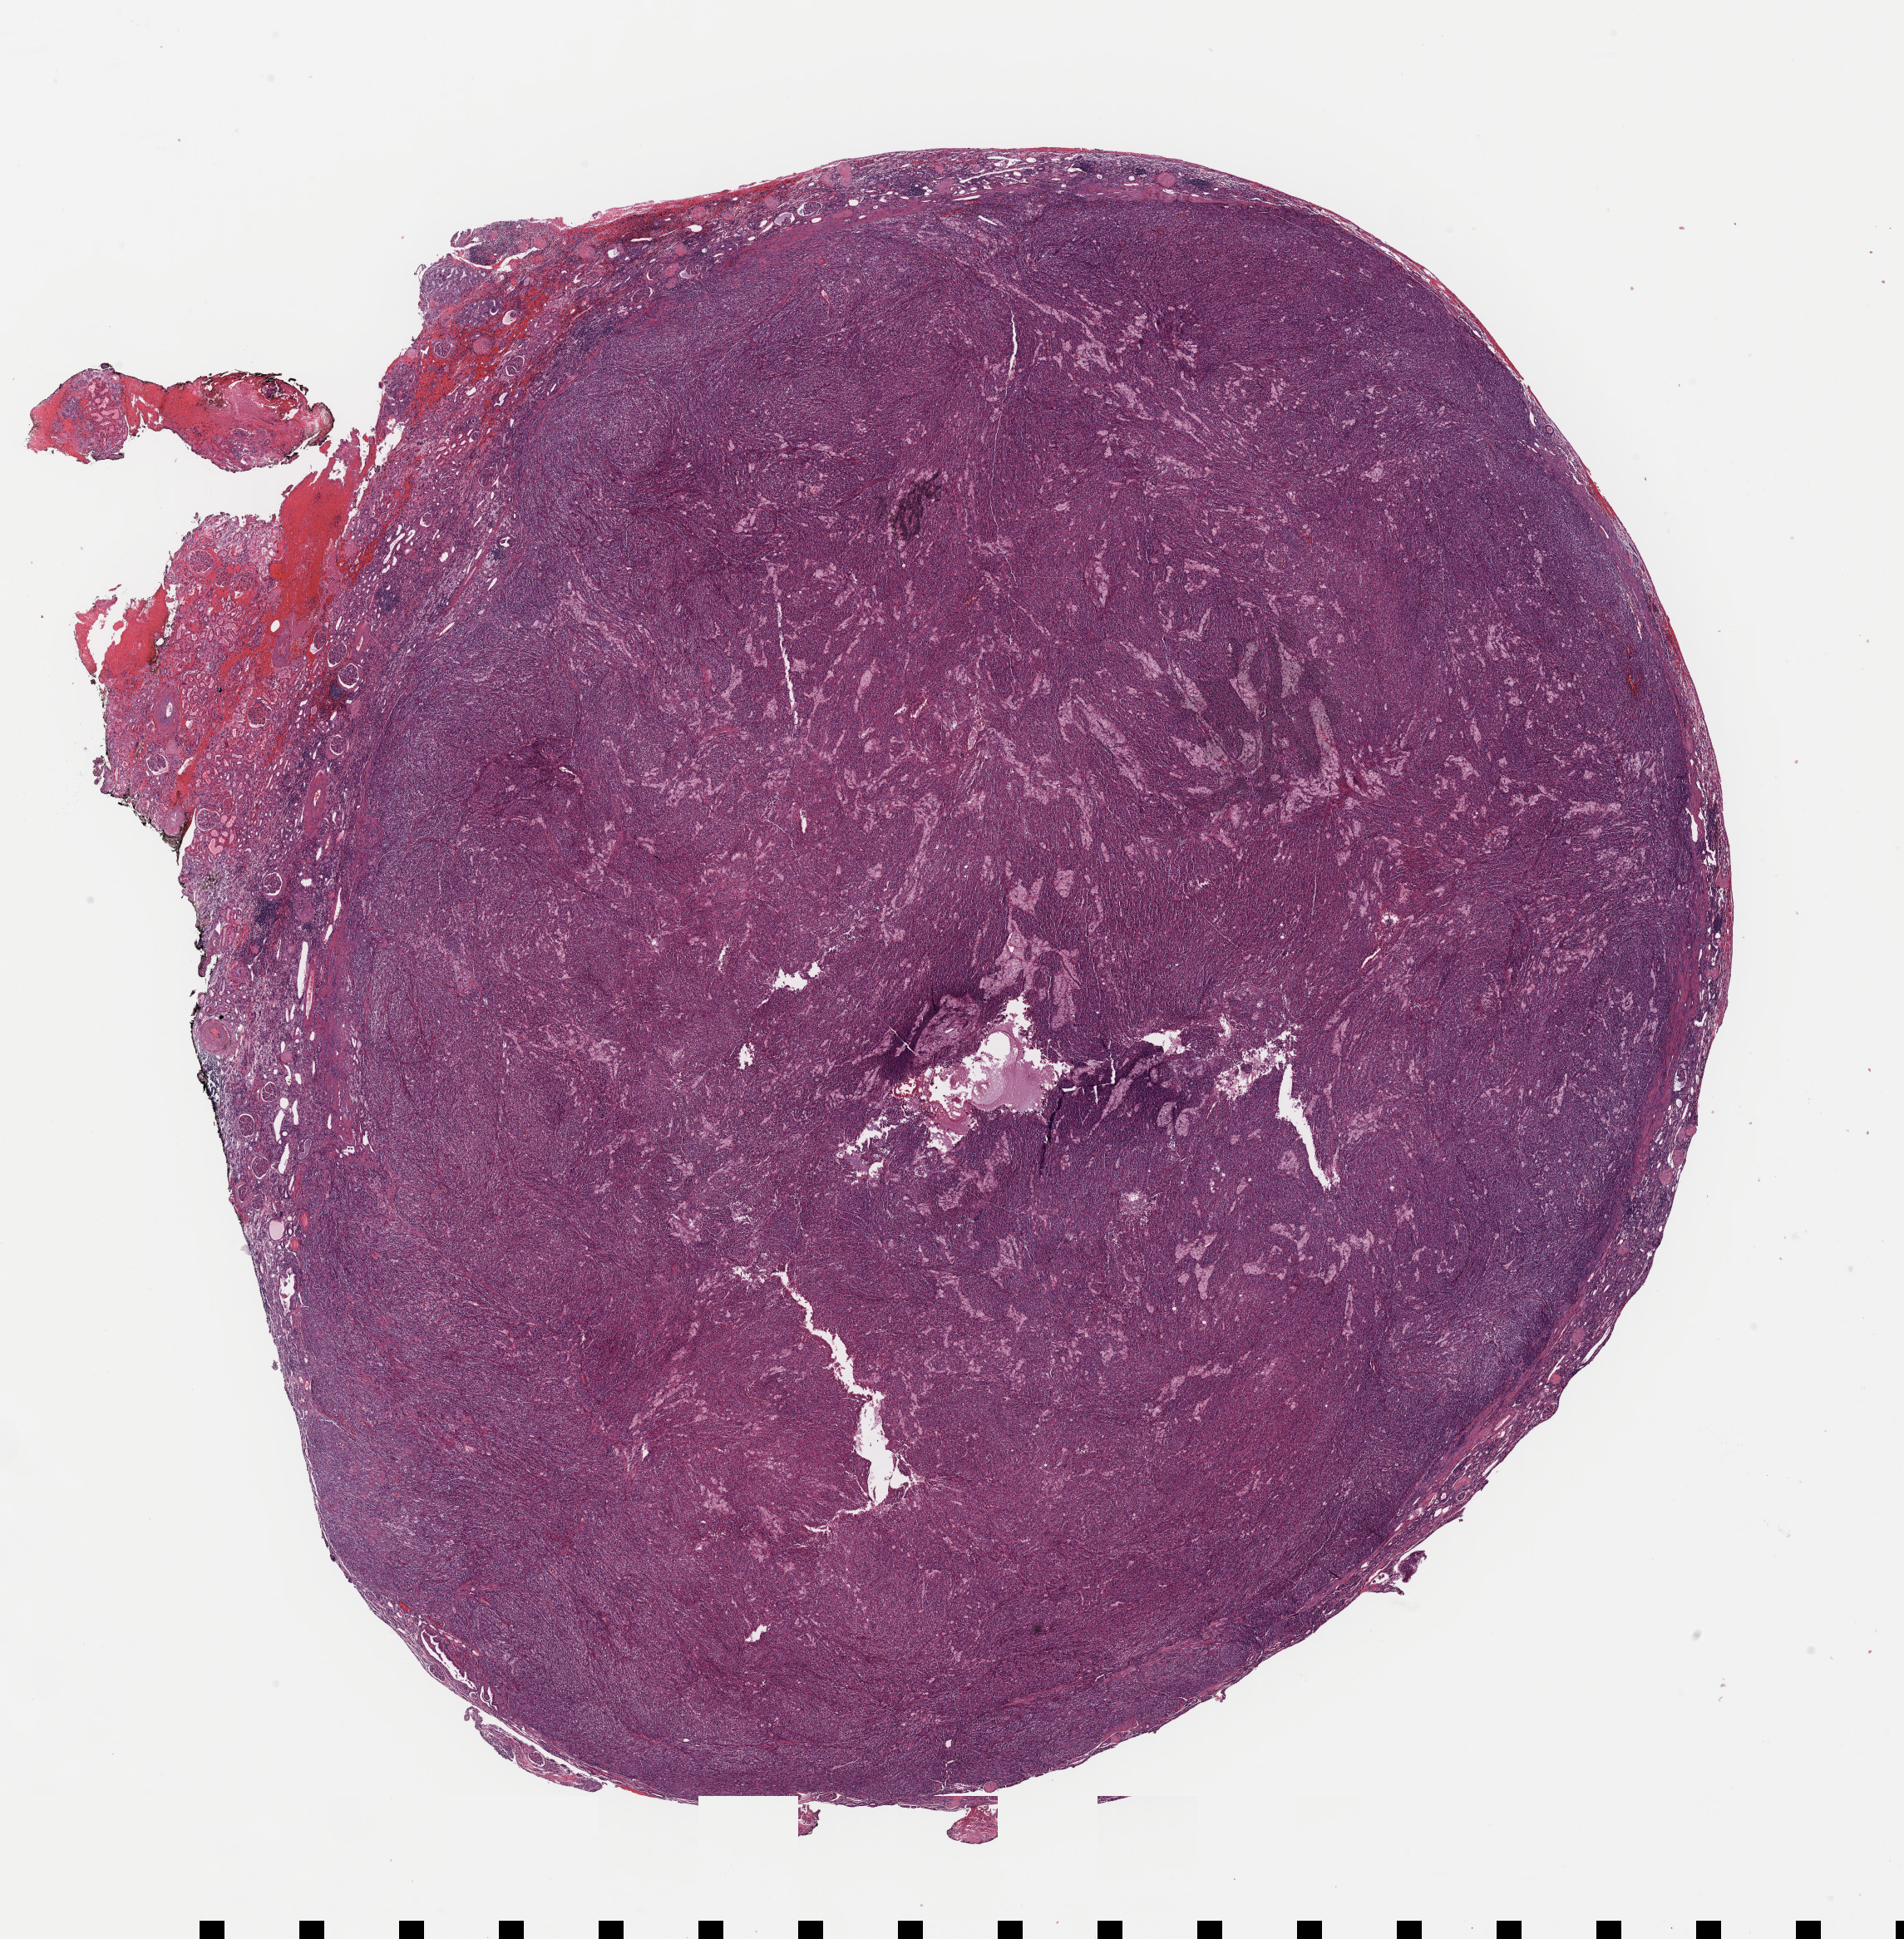
H&E-stained whole-slide image — whole scanned area (about 18.1 x 18.4 mm, slide scanned at 40x) shown as a low-resolution overview; formalin-fixed paraffin-embedded (FFPE) diagnostic section; kidney, primary tumour sample. Patient: female, age at initial diagnosis 60 years.
AJCC pathologic stage: I (7th edition). Pathologic diagnosis: Papillary adenocarcinoma, NOS.